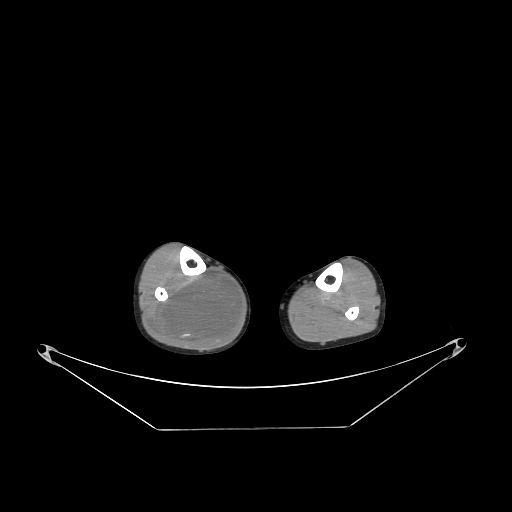
CT of an extremity soft-tissue mass (from a PET/CT study), one axial slice. Slice 98 of 267 in the series (ordered by position). Reconstruction kernel STANDARD. 140 kVp. Soft-tissue window (W 400 / L 40 HU). 3.75 mm slice thickness. 512 × 512 image matrix, field of view 500 × 500 mm. Male patient. From the clinical record (not read from this slice): histological type: liposarcoma - round cell; grade: high; site of the primary tumour: right calf.
Structures marked on this image (expert contour drawn on MRI and transferred to this co-registered scan by the dataset authors):
- gross tumour volume (mass): bounding box (x1, y1, x2, y2) in pixels: (151, 270, 241, 350)